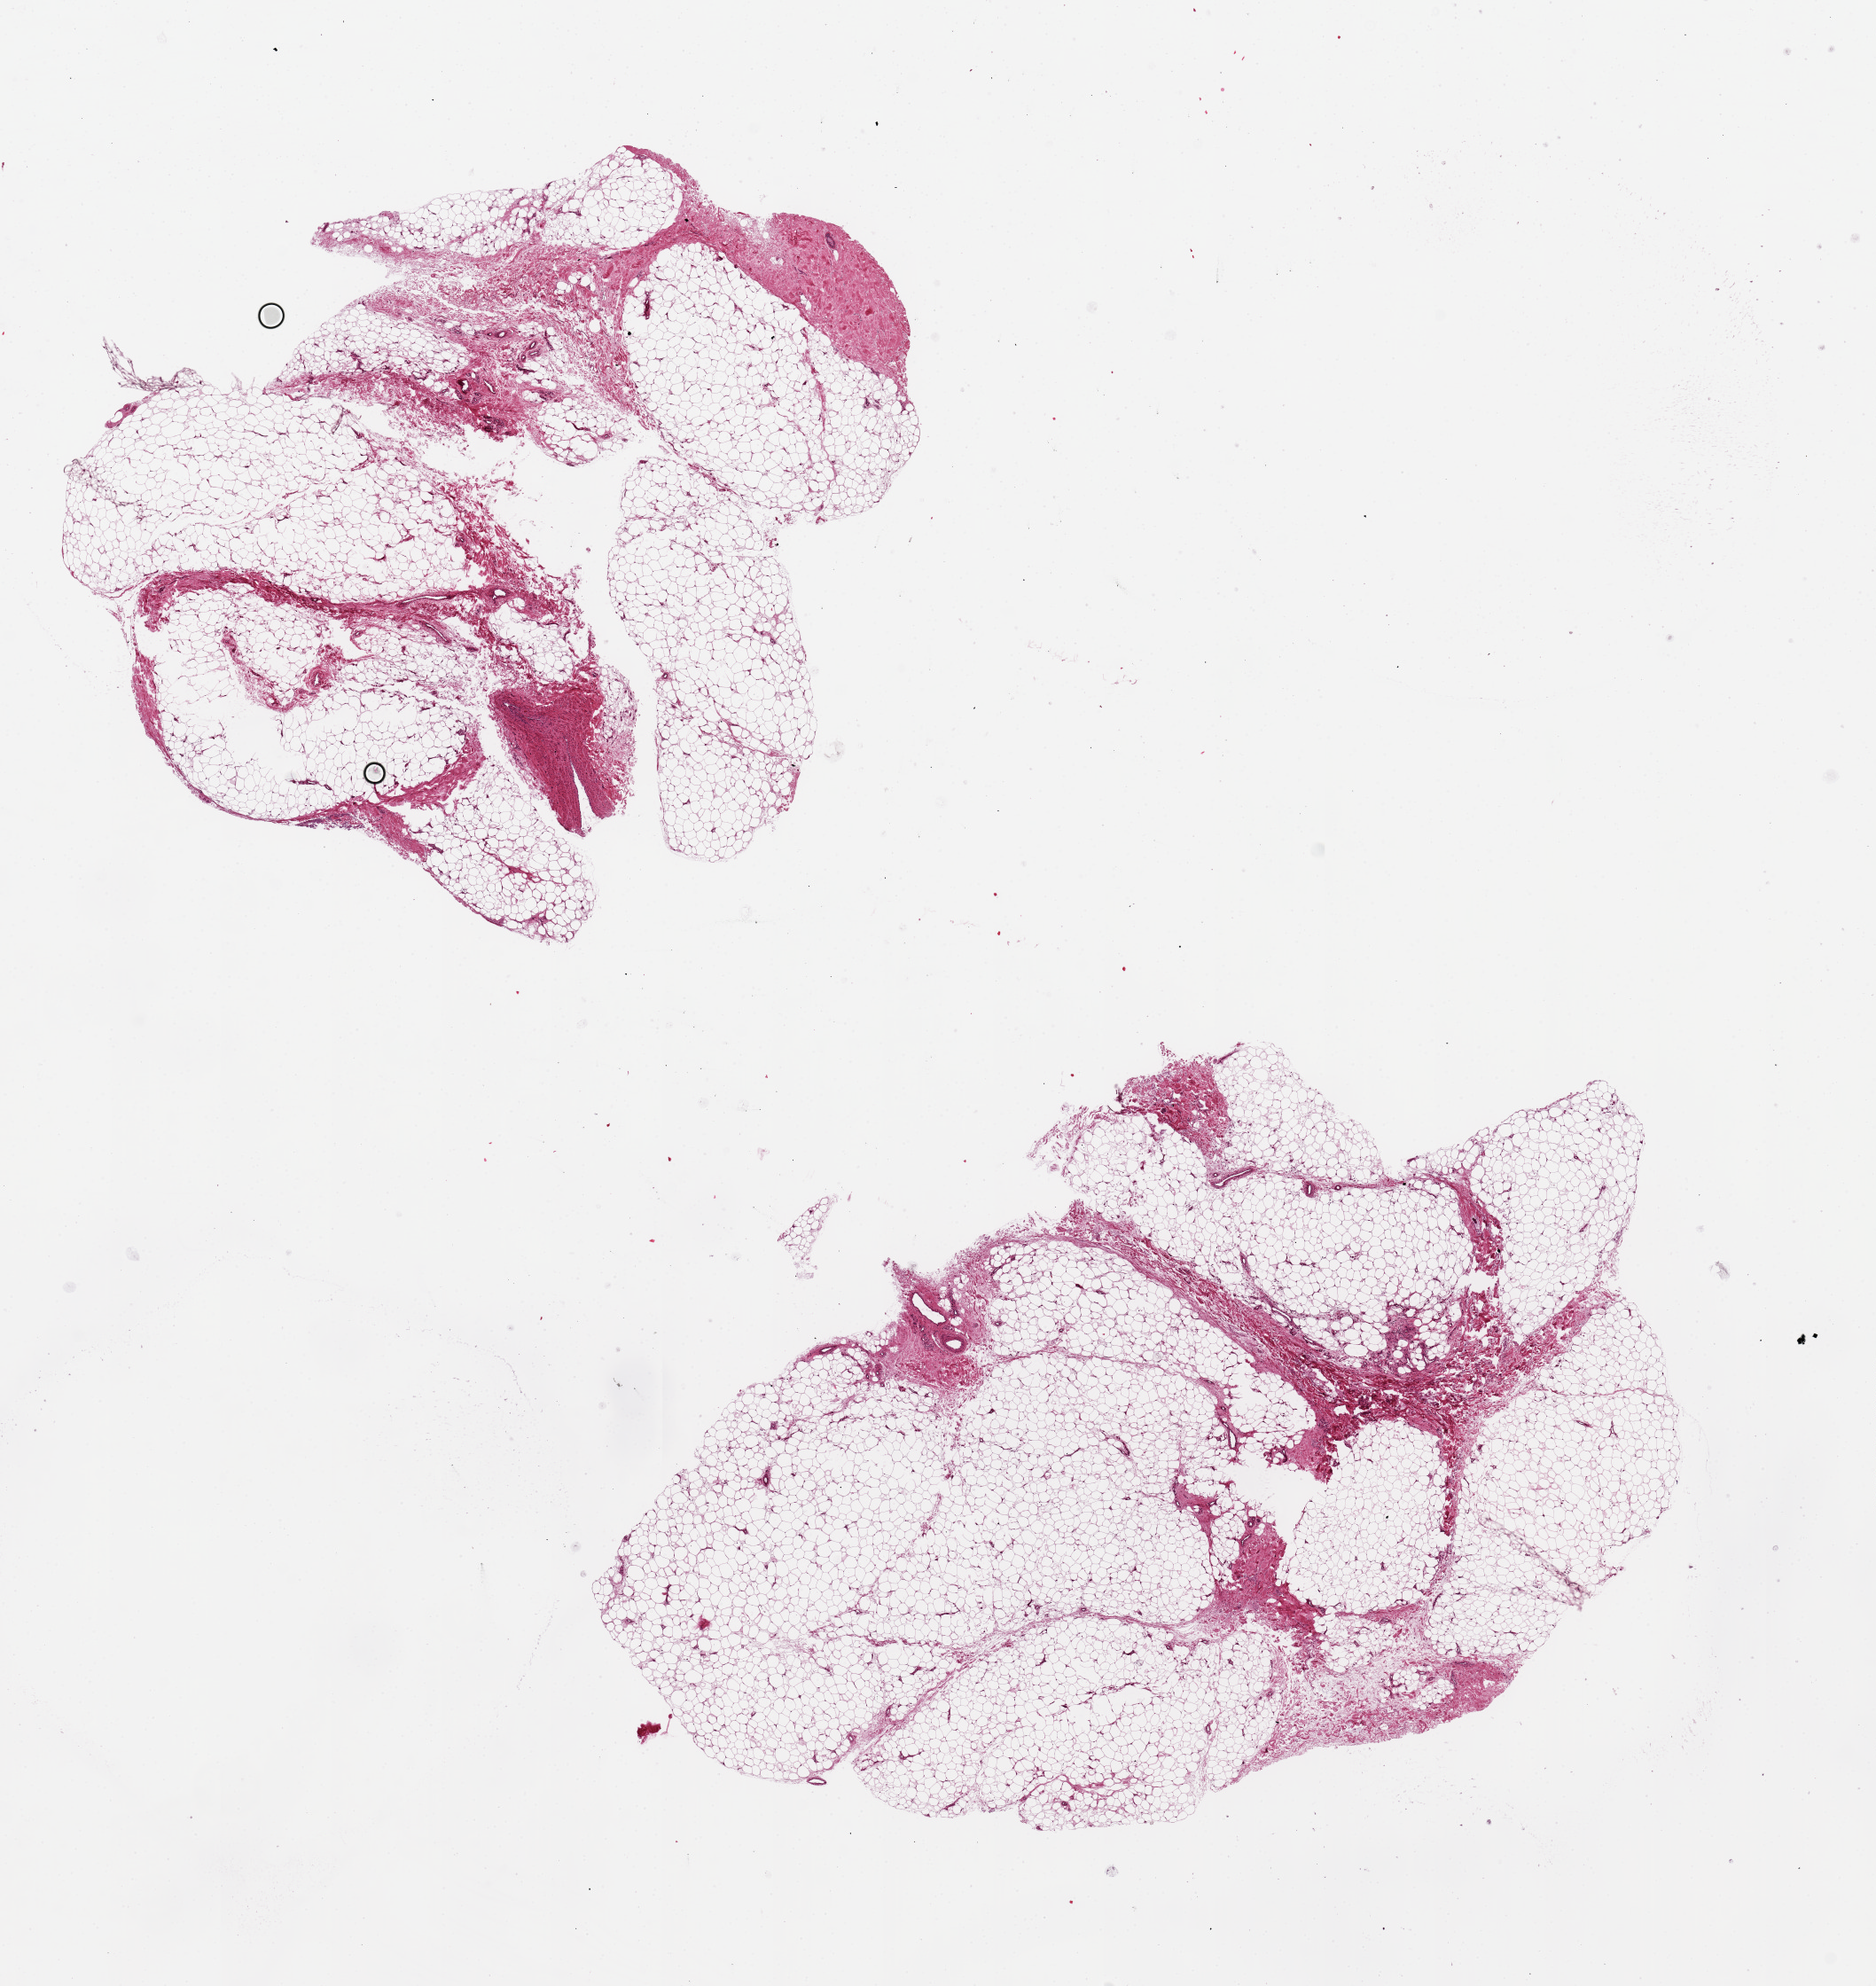
Whole-slide image, hematoxylin and eosin (H&E) stain — low-resolution overview of the scanned area, about 16.7 x 17.7 mm (from a 20x scan), PAXgene-fixed, paraffin-embedded tissue, sampled site (target tissue): adipose tissue, donor tissue sample. Male donor.
Review note (as recorded): 2 pieces ~8x2mm.